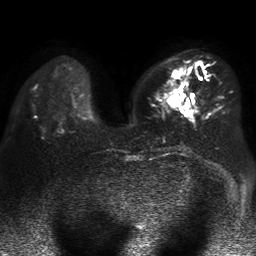
Breast MRI, one axial slice. Slice 18 of 50 in the series (ordered by position). Diffusion-weighted series; image 2 of 4 stored at this slice position (different b-values; order by instance number). 1.5 T. 4 mm slice thickness. 256 × 256 image matrix, field of view 360 × 360 mm. Female patient.
Outlined on this slice (outlined manually by an expert reader):
- tumour on diffusion-weighted imaging: bounding box [x1, y1, x2, y2] px = [168, 70, 185, 106]